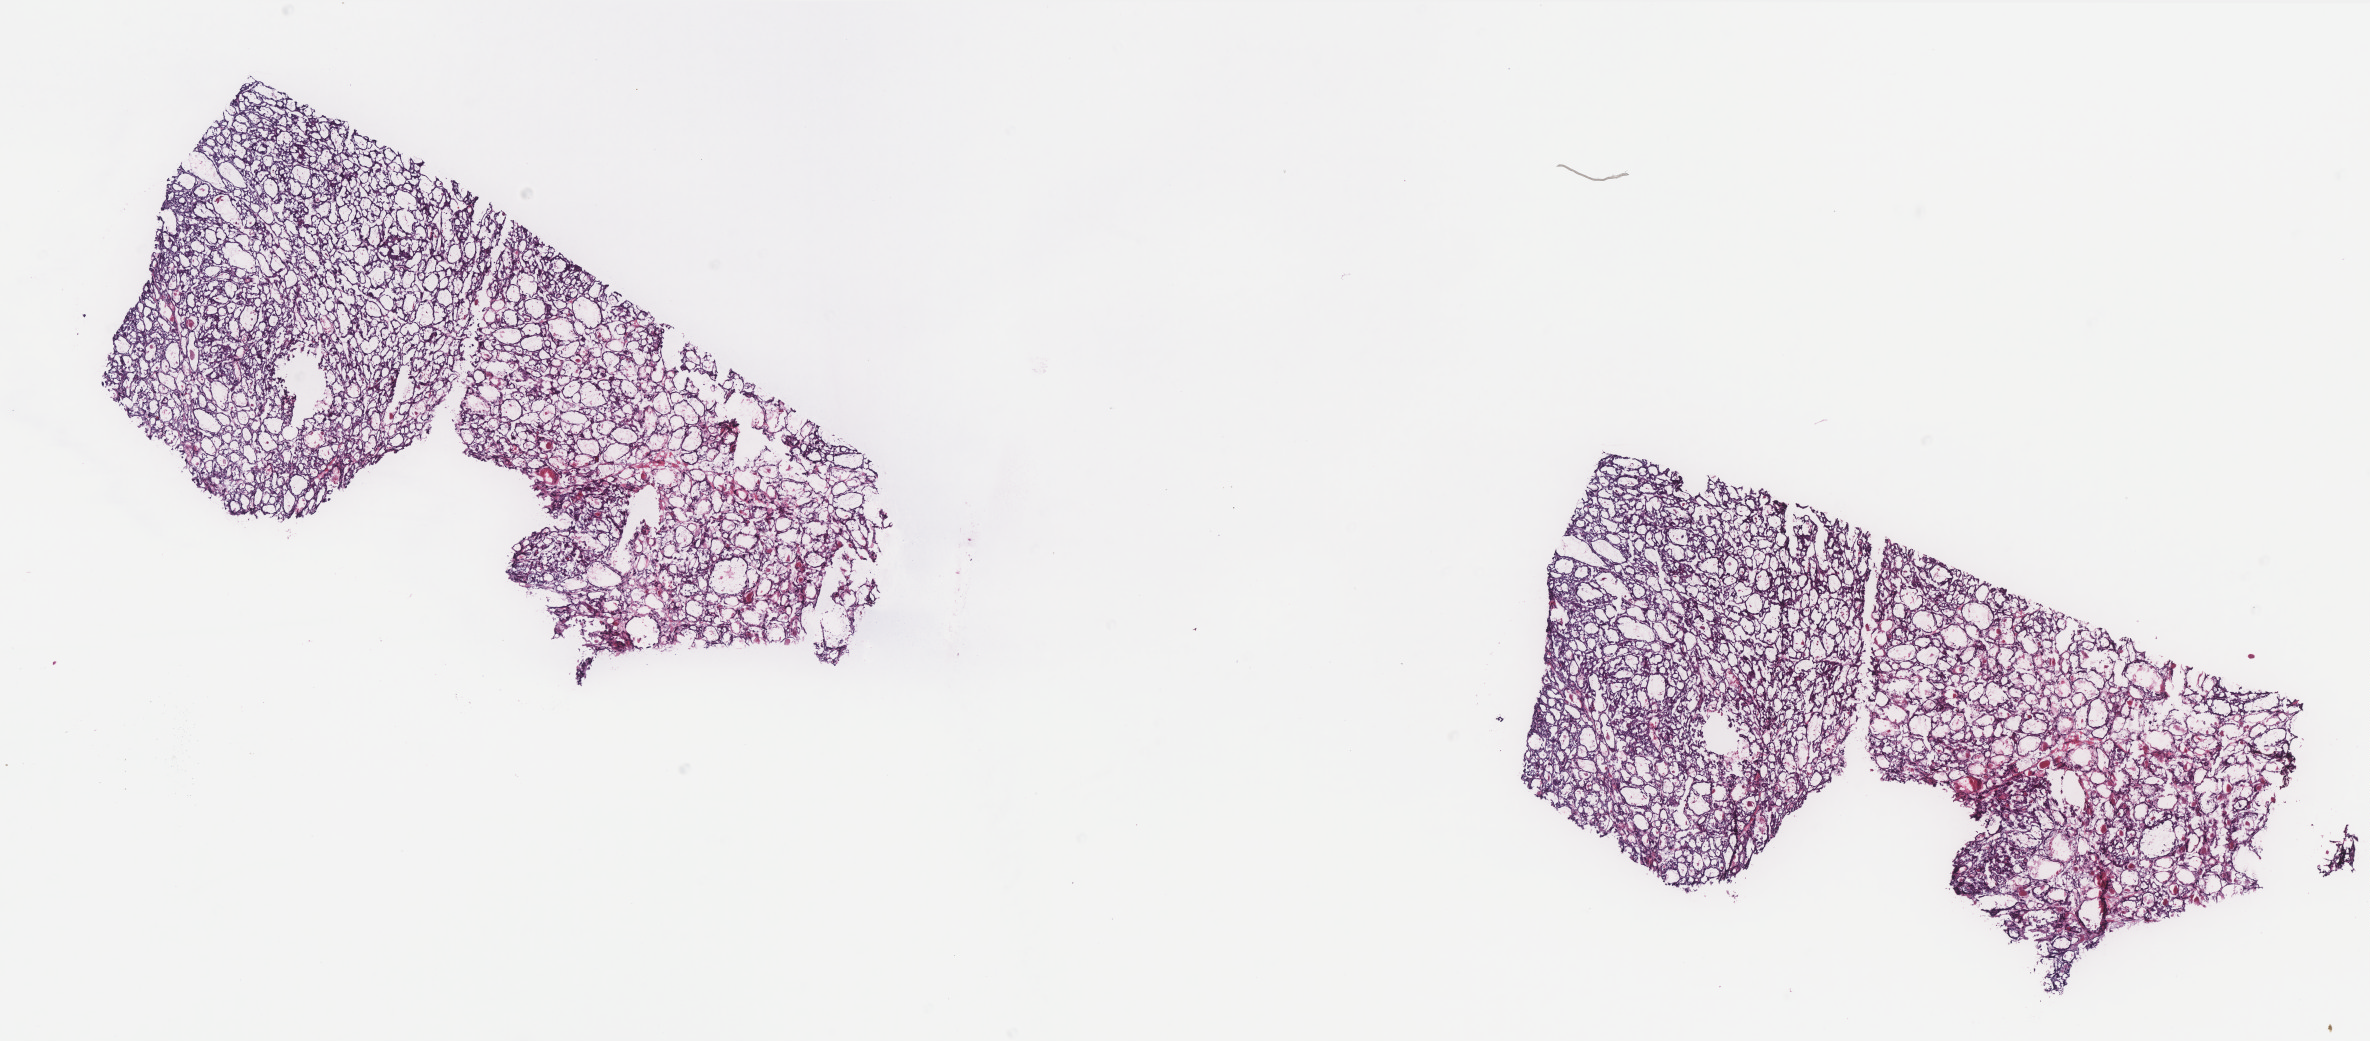
Whole-slide histology image, H&E, shown as a low-resolution overview of the whole scanned area (about 19.0 x 8.3 mm, from a 40x scan). Frozen section. Sample: primary tumour, thyroid. Male, age 65 years at initial diagnosis. Pathologist review of this section (percent, as recorded): tumour cells 100%, tumour nuclei 98%, normal cells 0%, stromal cells 0%, necrosis 0%. Infiltration values recorded for this section: lymphocyte infiltration 0%, monocyte infiltration 0%, neutrophil infiltration 0%.
* AJCC pathologic stage: II (6th edition)
* histologic diagnosis: Papillary adenocarcinoma, NOS (thyroid gland)